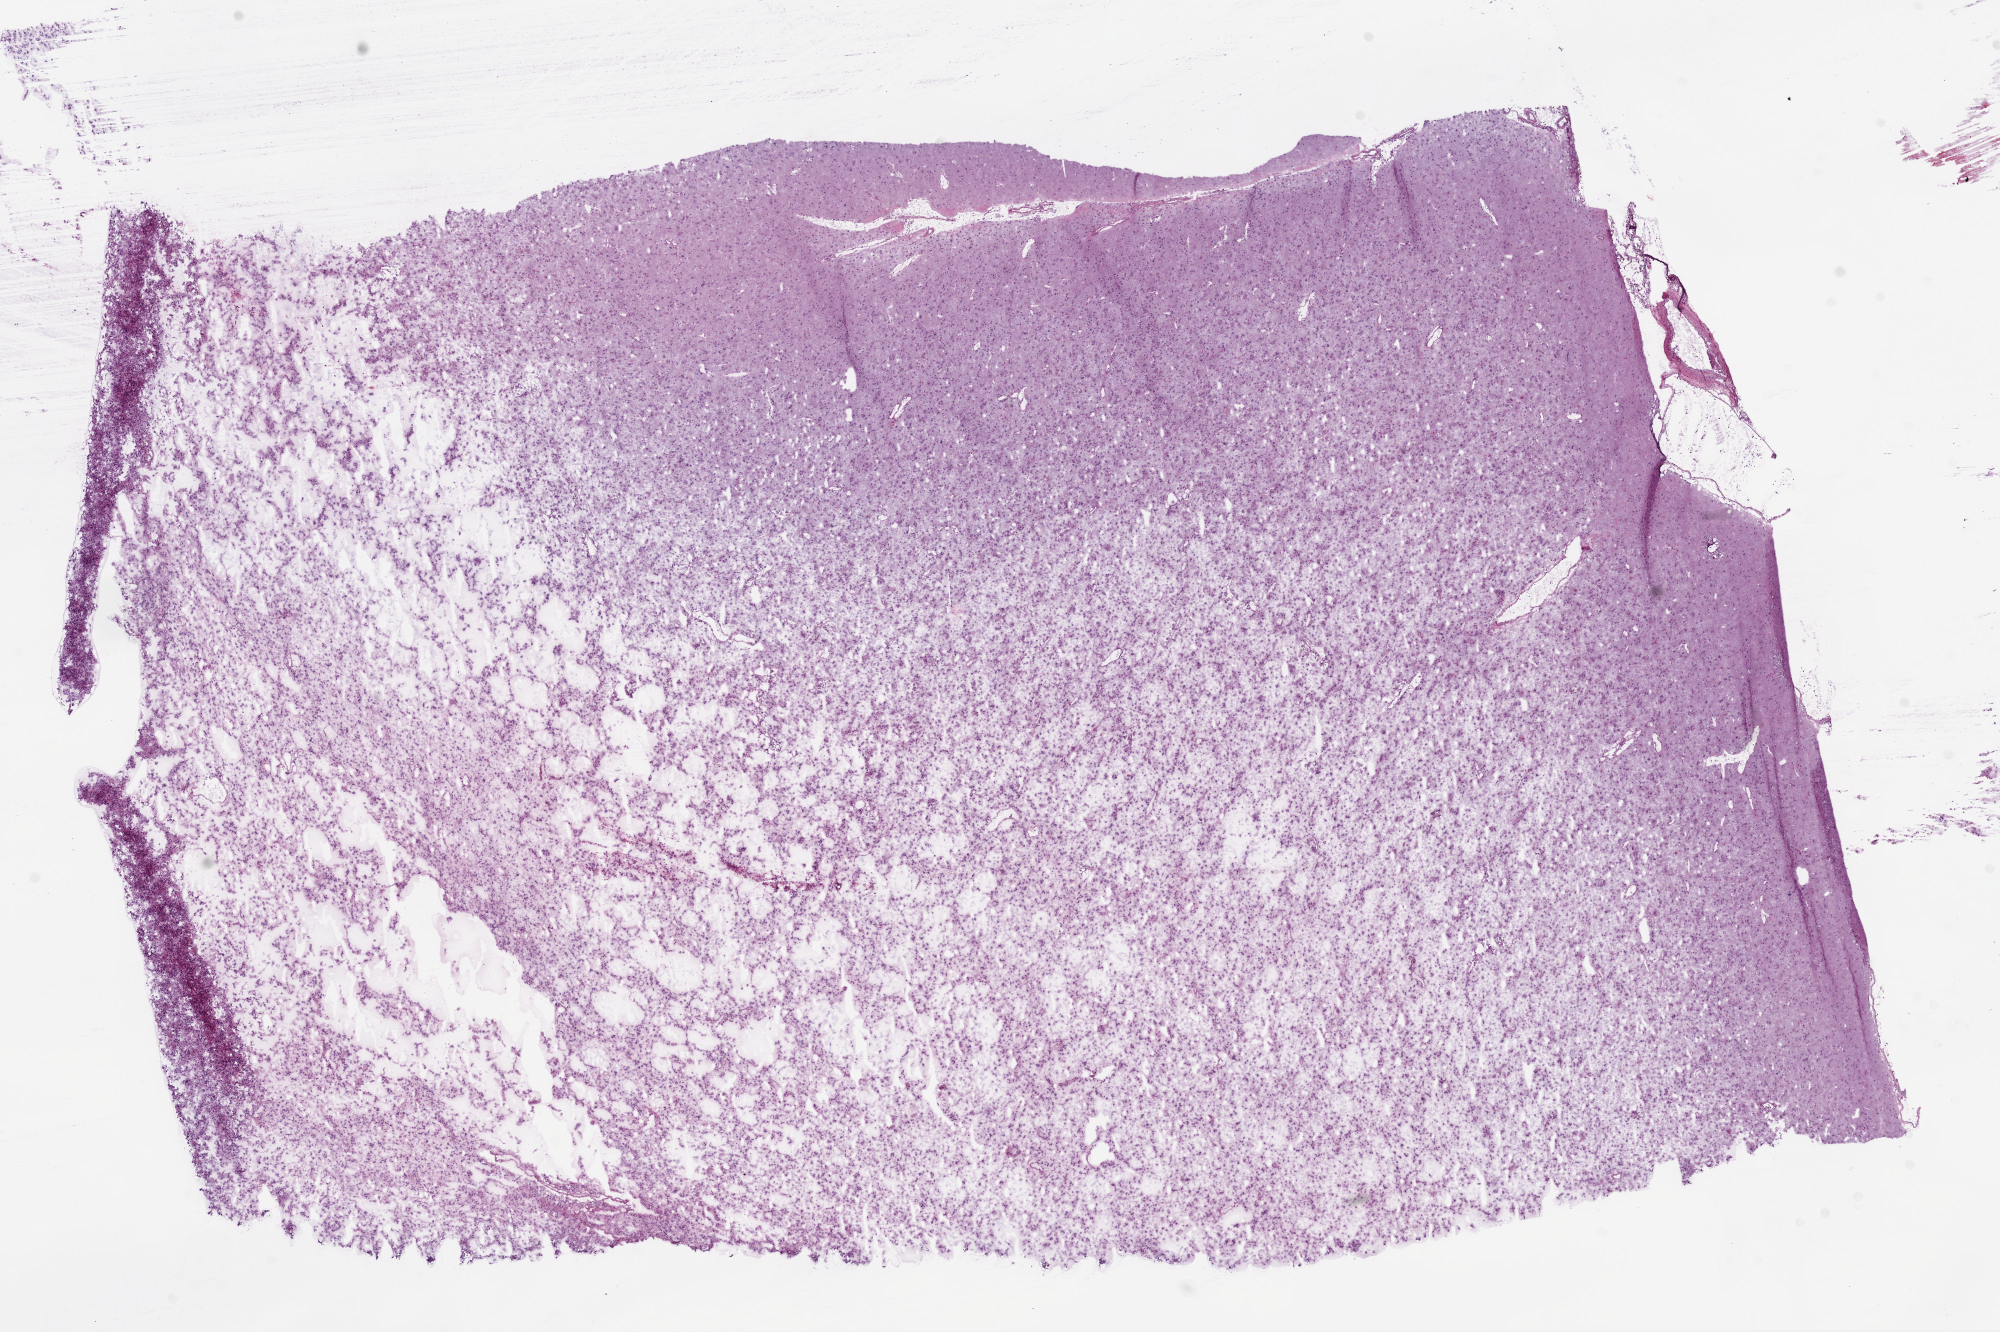
H&E-stained whole-slide image — shown as a low-resolution overview of the whole scanned area (about 16.0 x 10.7 mm, acquisition: 20x scan); frozen section from the bottom of the tissue portion; primary tumour sample from the brain. Male, age 61 years at initial diagnosis.
Pathologic diagnosis: Mixed glioma (cerebrum).